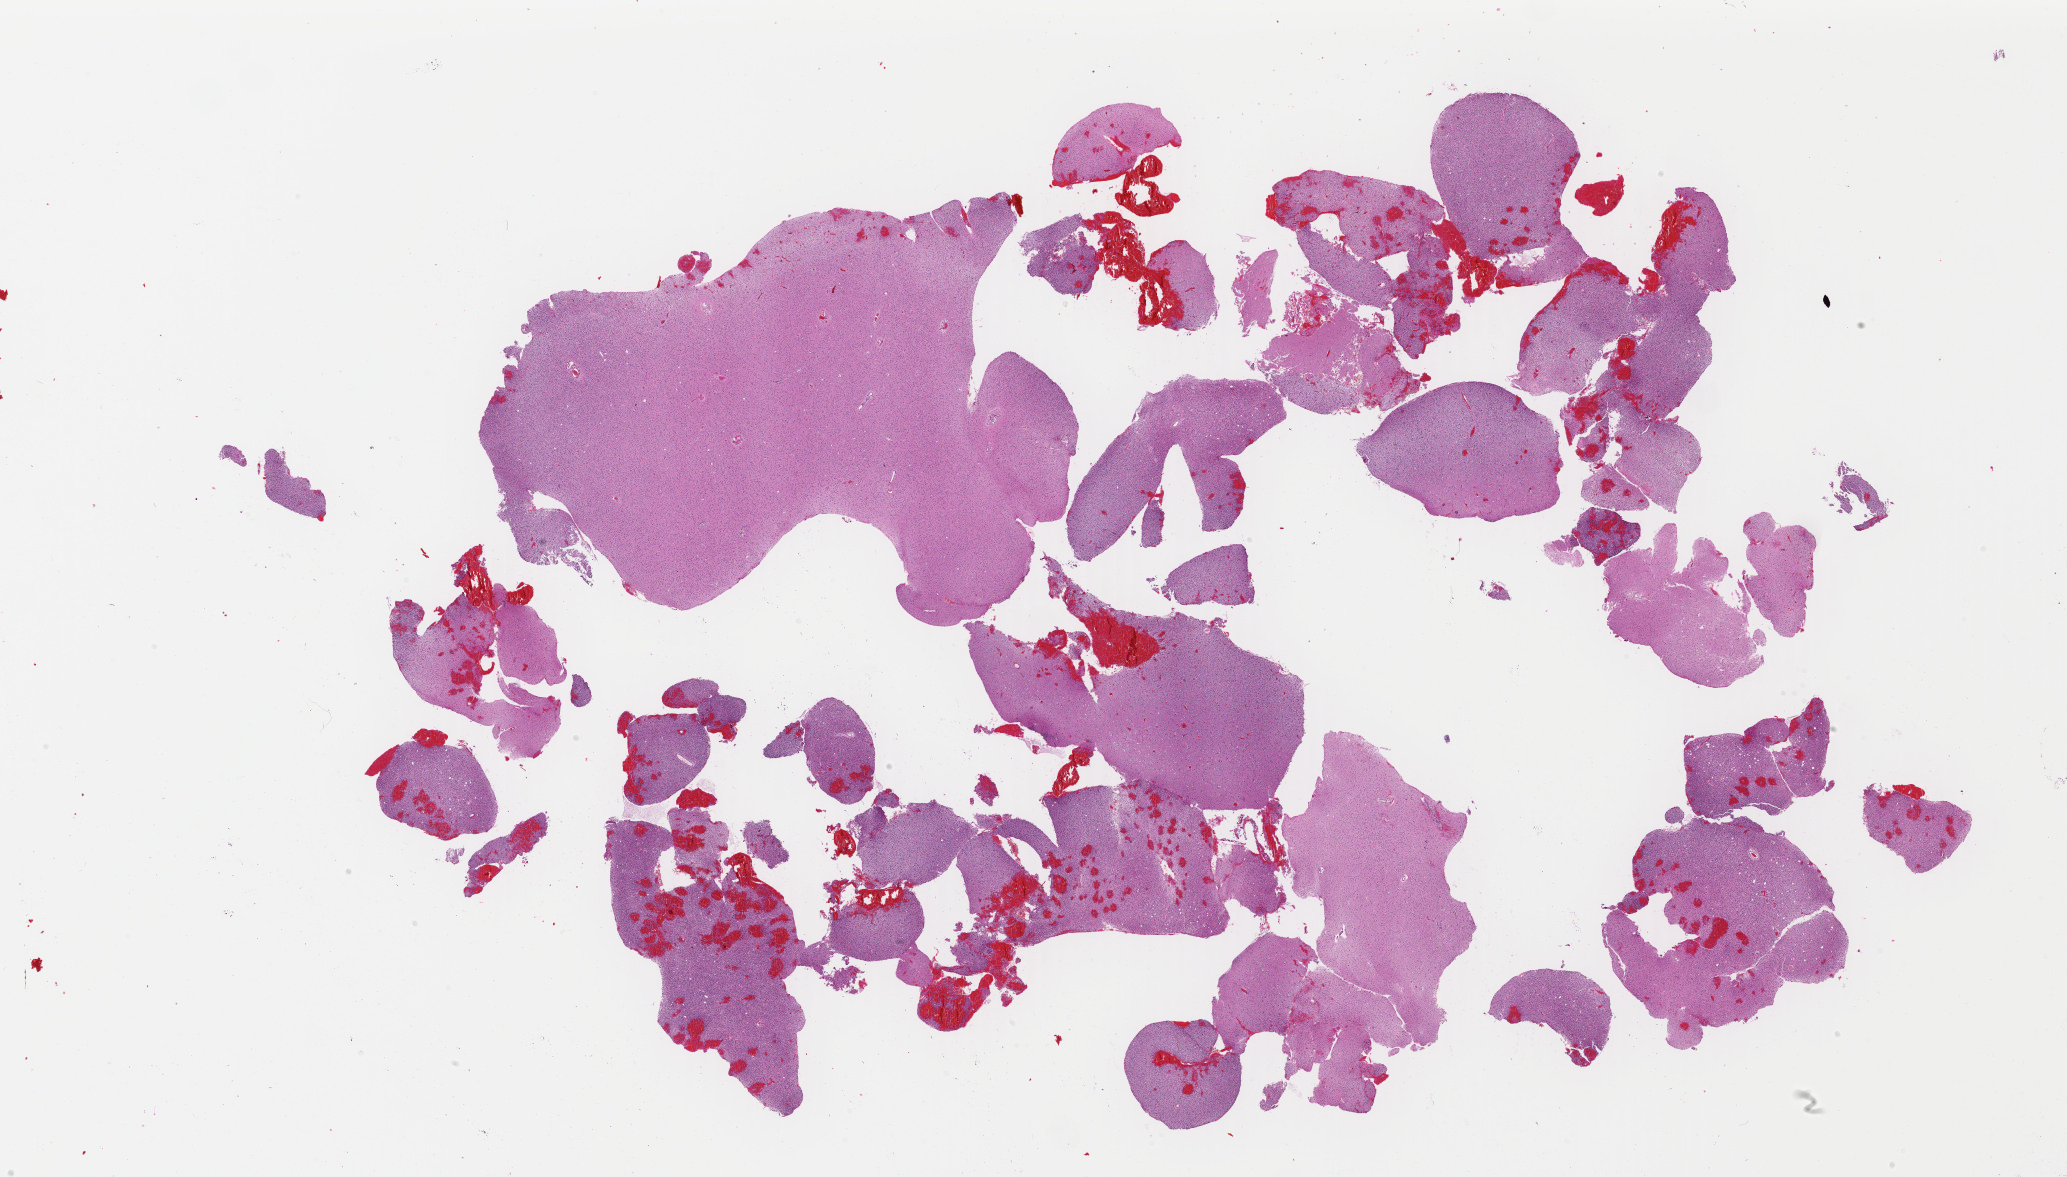
H&E-stained whole-slide image — whole scanned area (about 32.5 x 18.5 mm, from a 40x scan) shown as a low-resolution overview. Formalin-fixed paraffin-embedded (FFPE) diagnostic section. Sample: primary tumour, brain. Female patient; age at initial diagnosis 34 years. Histologic grade: G2 (moderately differentiated).
* laterality: right
* pathologic diagnosis: Mixed glioma (cerebrum)